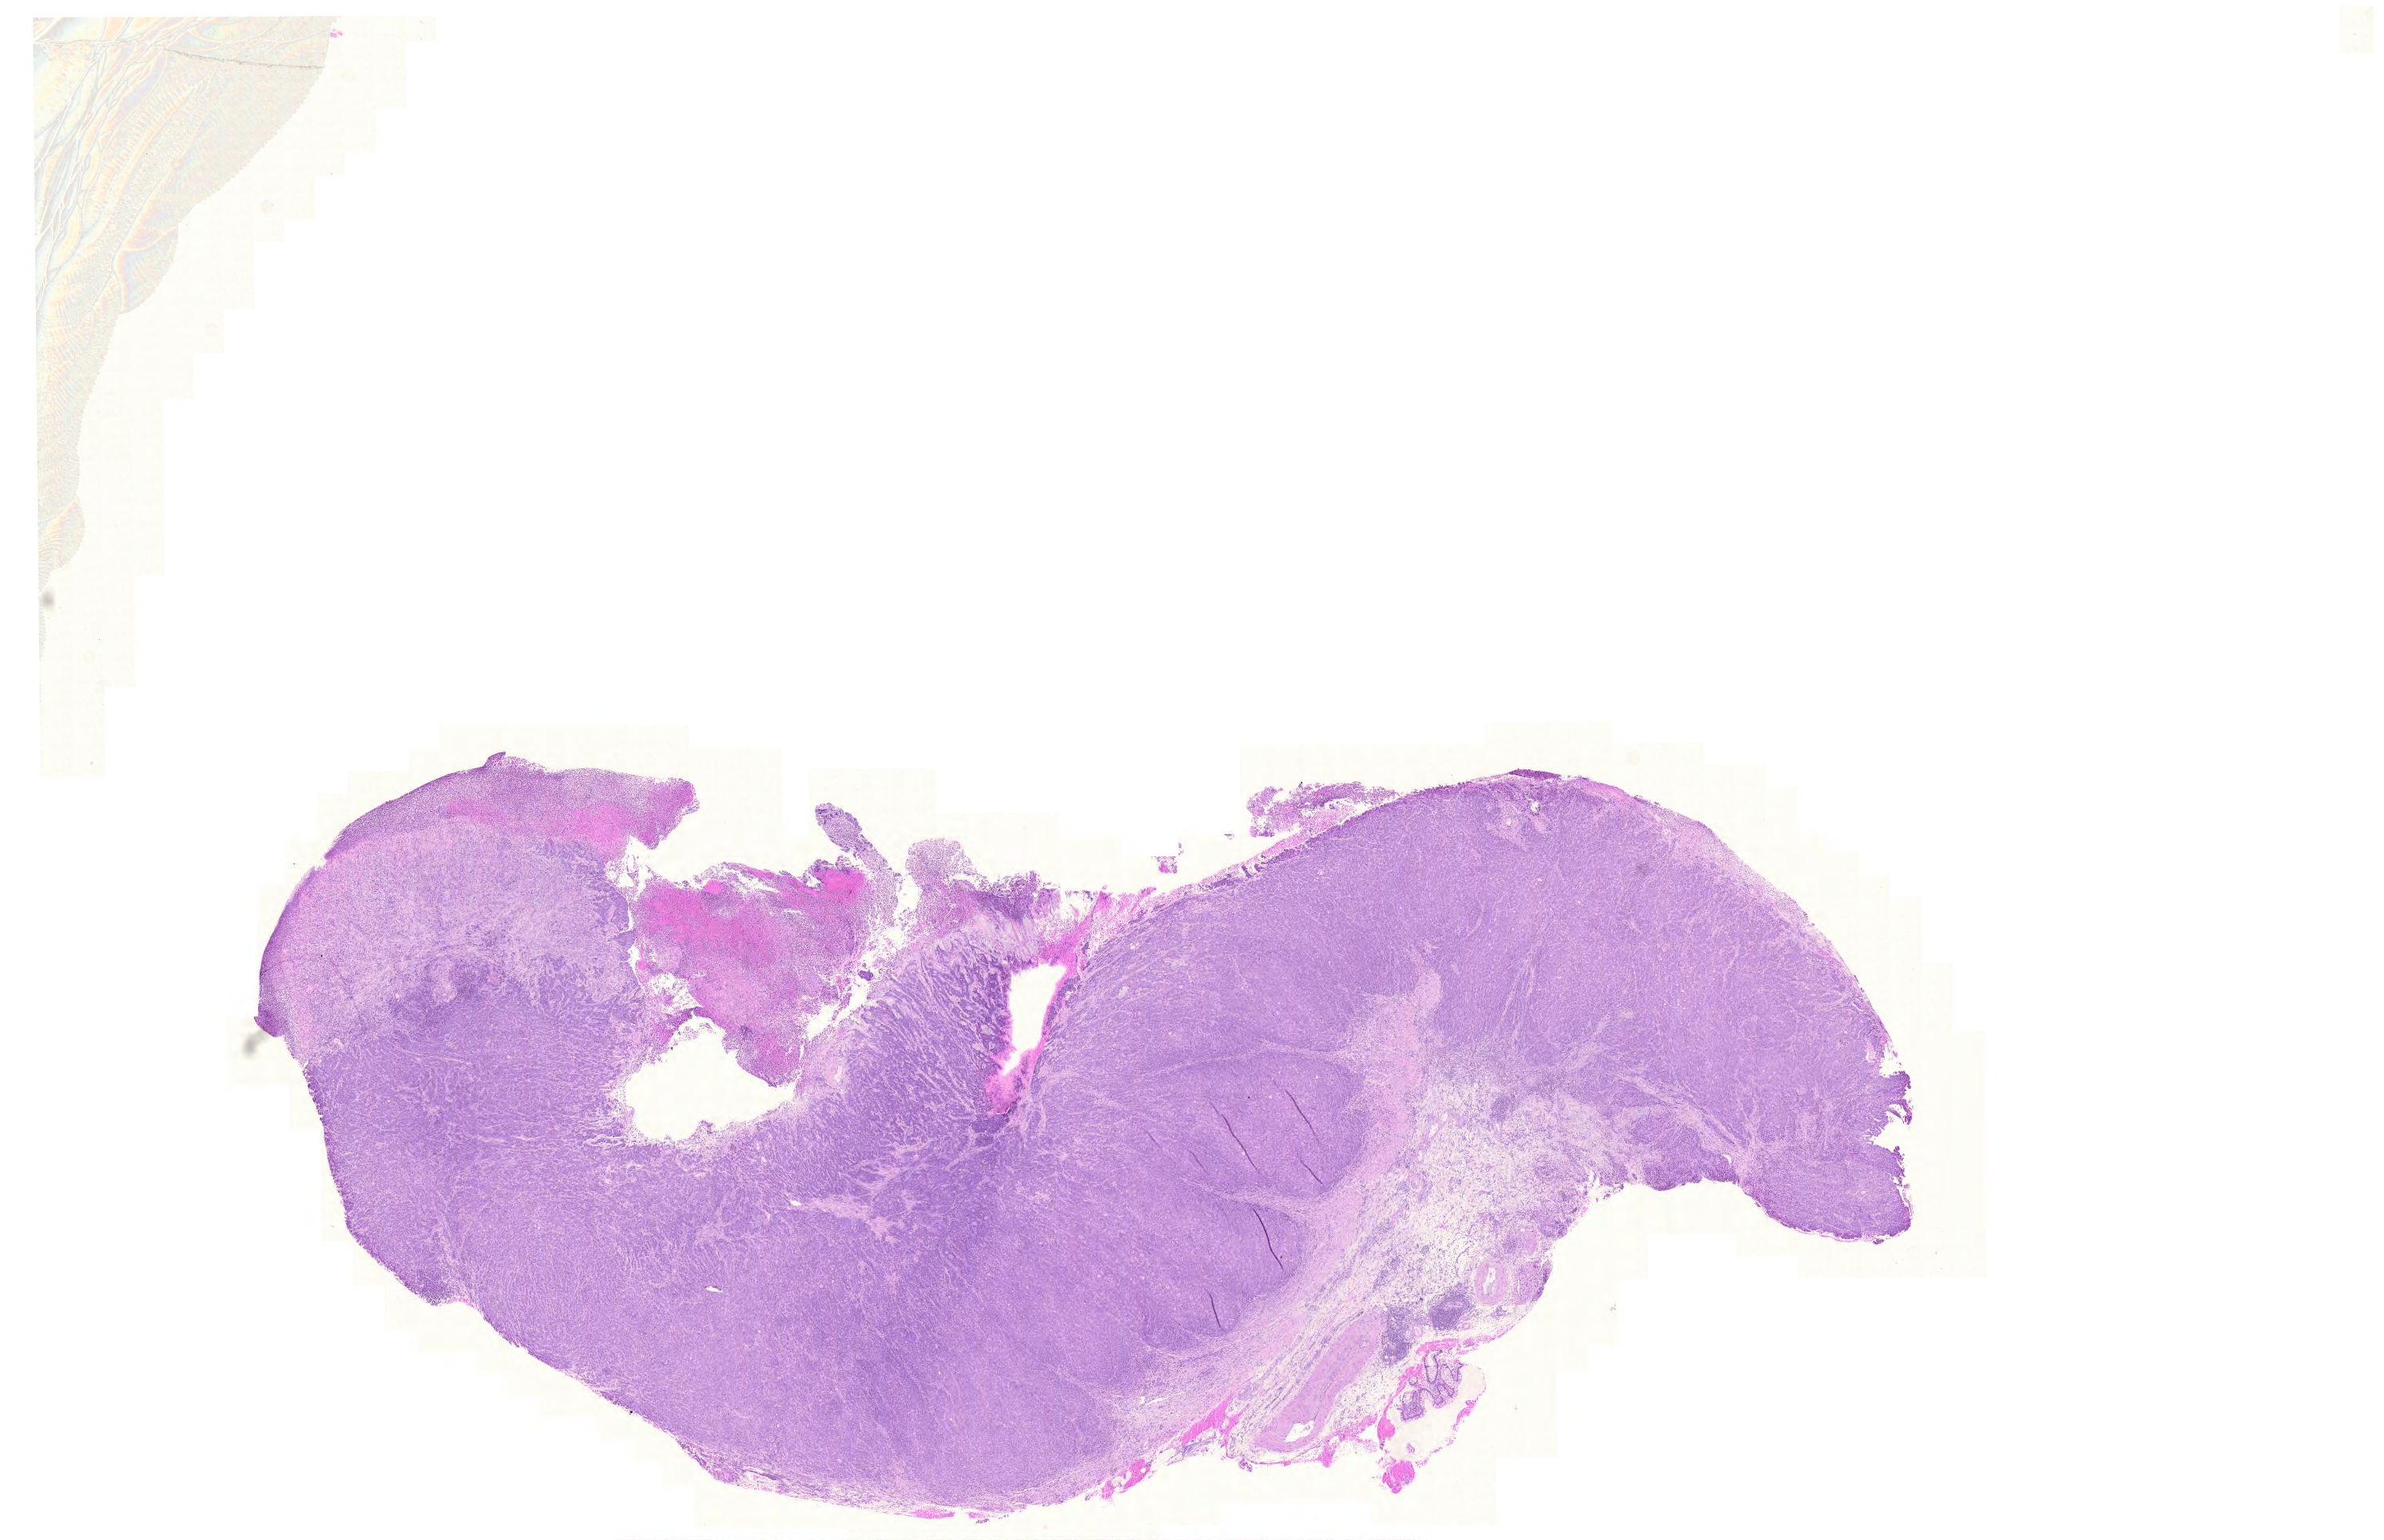
Hematoxylin and eosin (H&E) stained whole-slide image — low-resolution overview of the scanned area, about 22.2 x 14.3 mm; formalin-fixed paraffin-embedded (FFPE) diagnostic section; primary tumour sample from the colon. Male patient; age at initial diagnosis 77 years.
Diagnosis: Adenosquamous carcinoma (ascending colon). AJCC pathologic stage: II (5th edition).